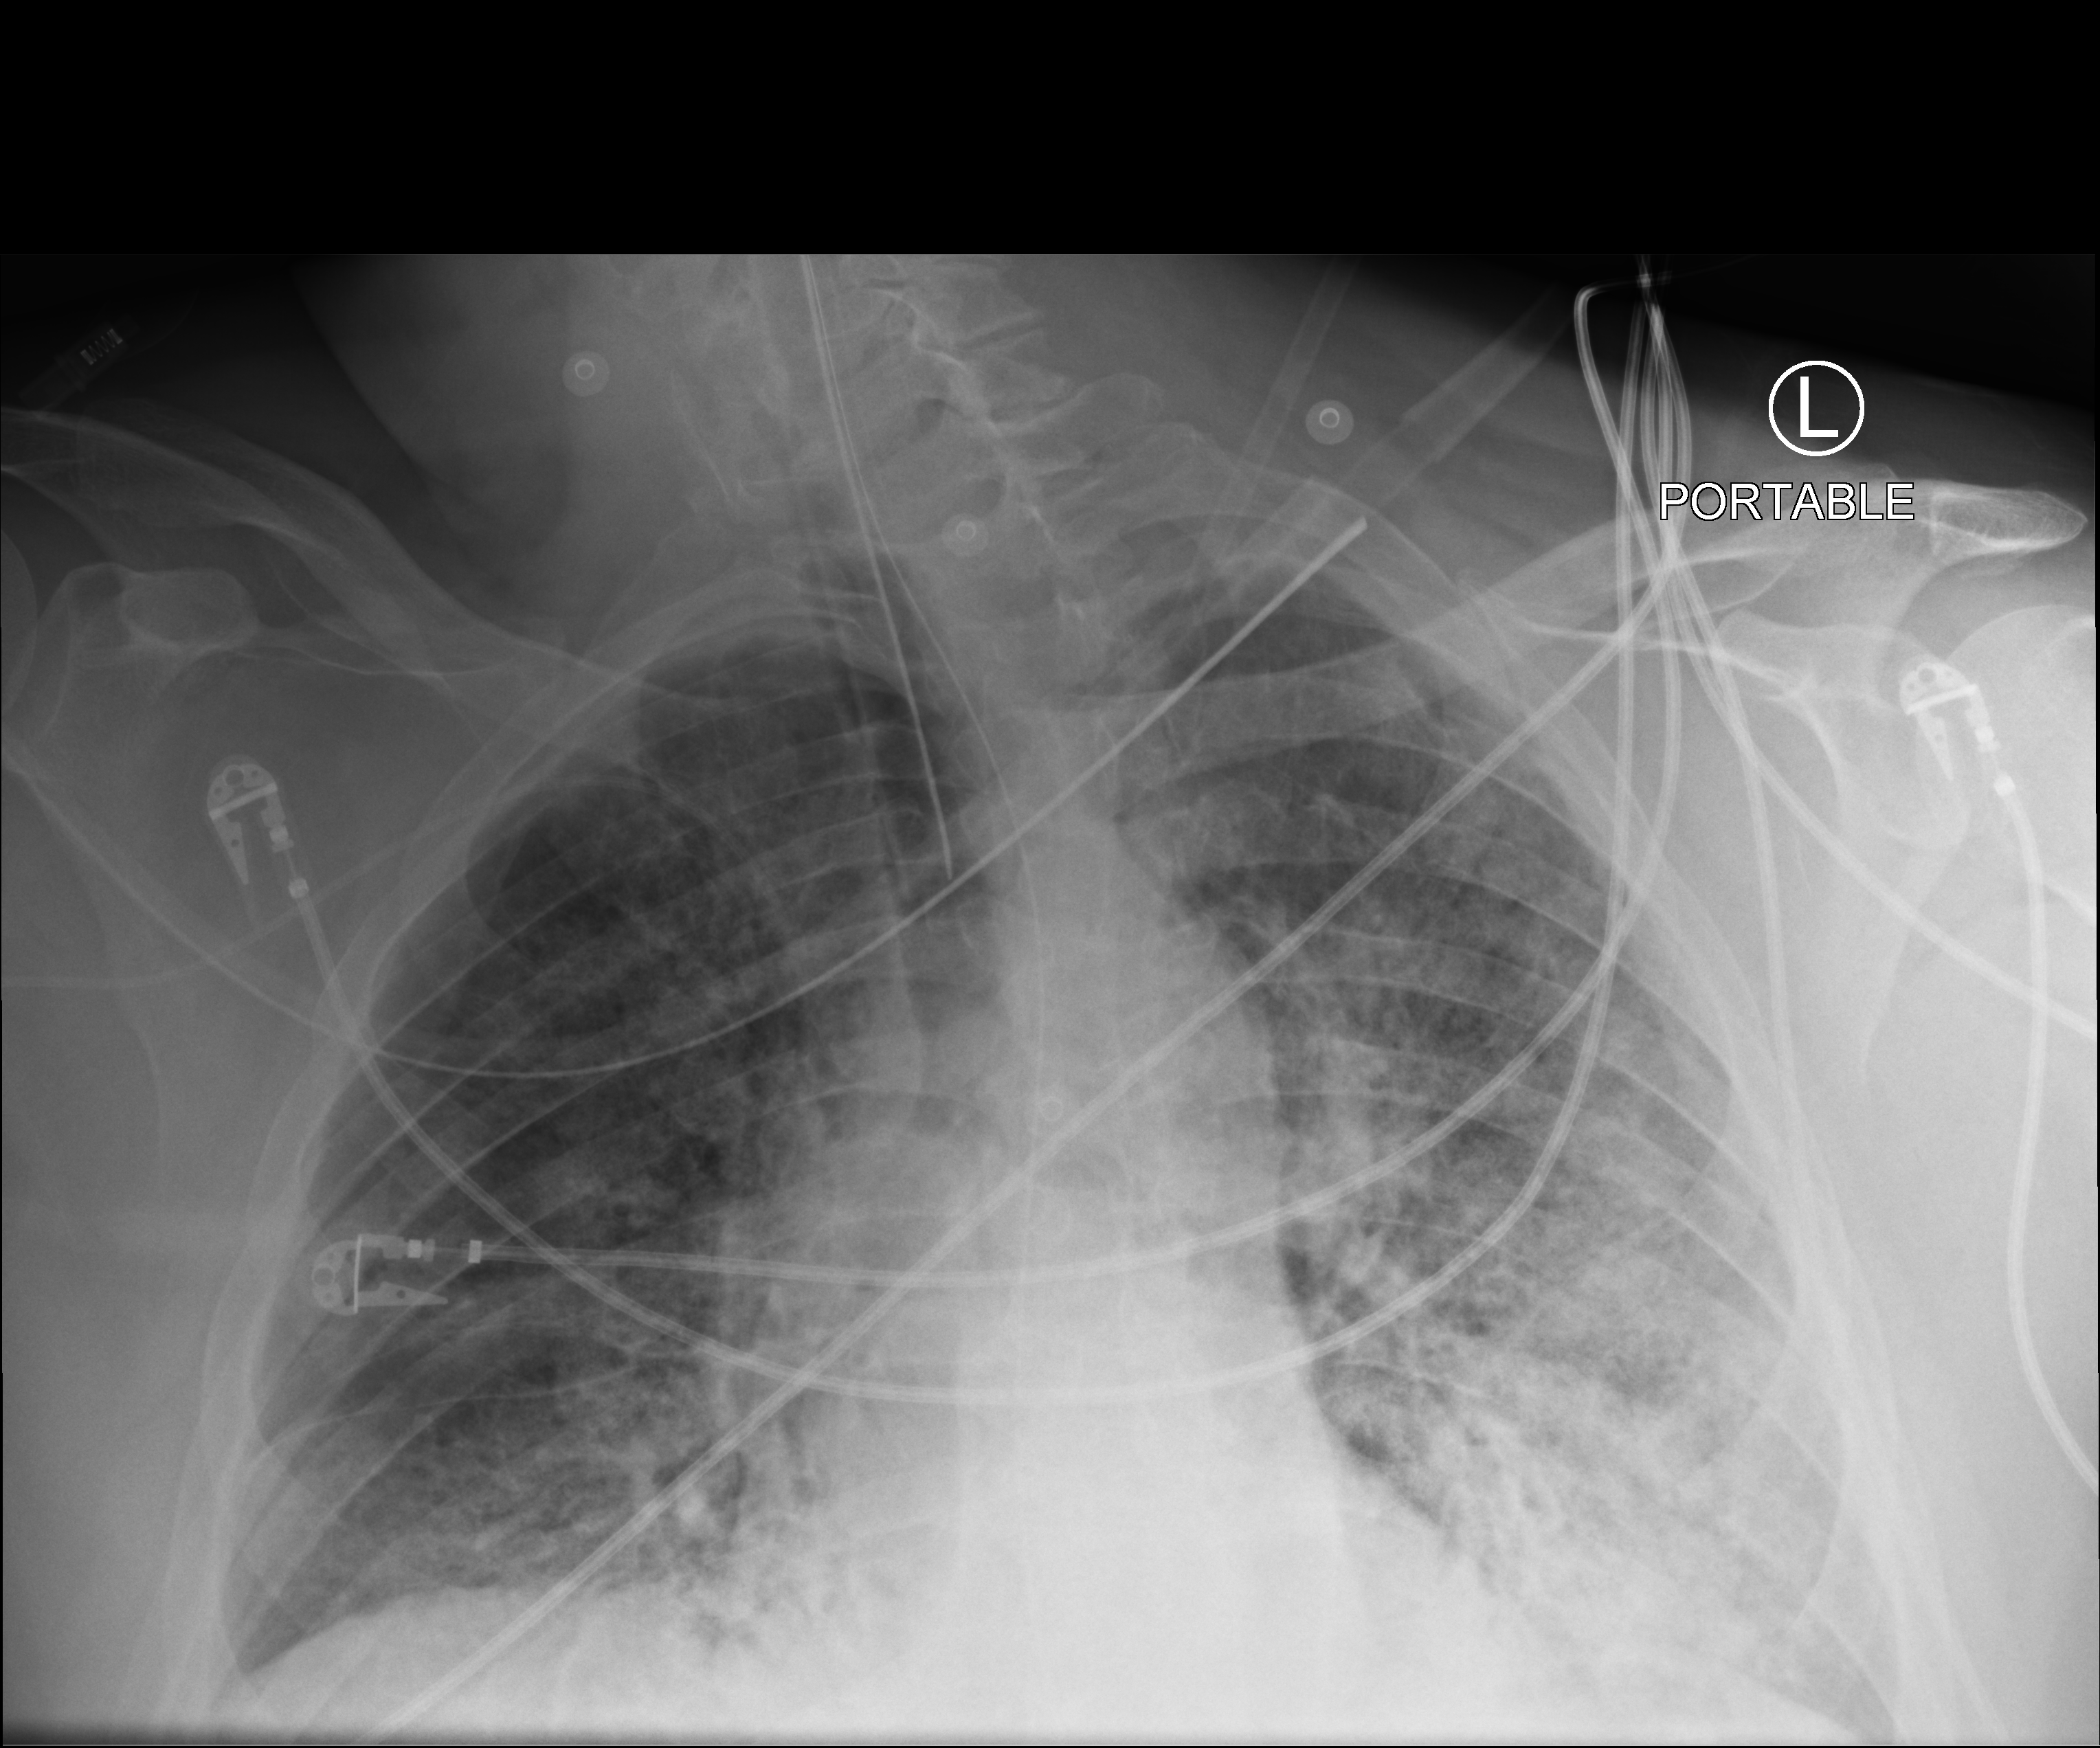
Portable chest radiograph. Patient hospitalised with COVID-19; male, aged 60–74 years.
Admission-level facts for this patient (not findings on this image; timing relative to this image not recorded): other chronic lung disease (admission record): yes; admitted to intensive care during this hospital stay: yes.